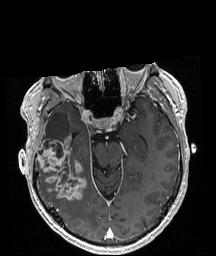
Brain MRI from a brain-tumour surgery series, one axial slice; position 125 of 208 along the scan axis; T1-weighted post-contrast; 216 × 256 image matrix. From the clinical record (not read from this slice): histopathology: Astrocytoma; WHO grade: 4; IDH mutation: yes; tumour location: Right Temporal.
Structures marked on this image (expert manual segmentation):
- tumour: bounding box <36,135,87,201> (left, top, right, bottom; pixels)